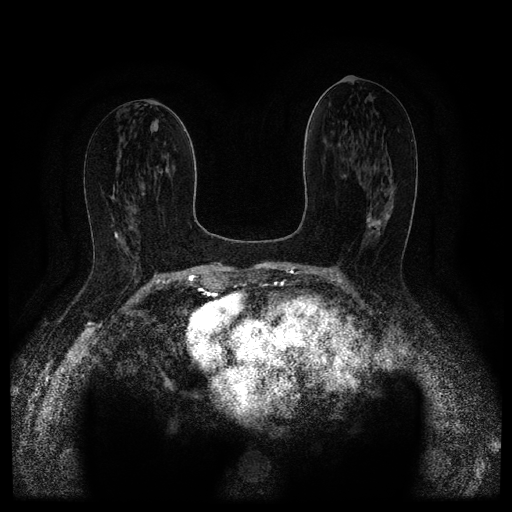
Breast MRI (dynamic contrast-enhanced, multi-phase), one axial slice; position 54 of 116 along the scan axis; dynamic contrast-enhanced series, time point 2 of 5 at this slice position (early post-contrast); 1.5 T; TE 2.6 ms, TR 5.4 ms; 2 mm slice thickness; 512 × 512 image matrix, field of view 340 × 340 mm. Patient: female, 67 years.
Outlined on this slice (semi-automatically segmented with operator editing):
- breast lesion (labelled 'tumour' in the annotation; benign lesions carry a separate 'benign' label): bounding box (x1, y1, x2, y2) in pixels: (366, 213, 390, 235)